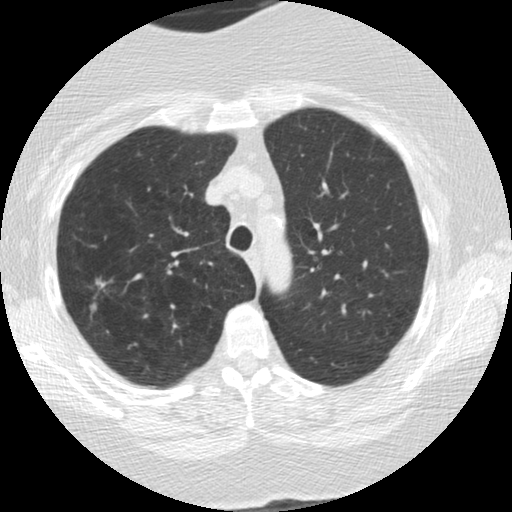
Low-dose screening chest CT, one axial slice; position 132 of 166 along the scan axis; lung window (W 1500 / L -600 HU); 512 × 512 image matrix, field of view 309 × 309 mm.
Outlined on this slice (outlined manually by an expert reader):
- lesion 1 (tumor, upper lobe of right lung): bounding box (x1, y1, x2, y2) in pixels: (90, 303, 98, 311)
- lesion 2 (tumor, upper lobe of right lung): (96, 276, 106, 287)